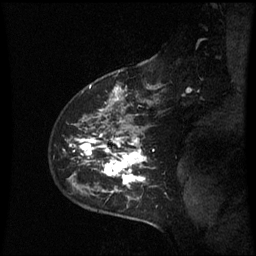
Breast MRI (dynamic contrast-enhanced), one sagittal slice; slice 46 of 60 in the series (ordered by position); dynamic contrast-enhanced series, image 2 of 3 at this slice position (ordered by acquisition); 1.5 T; TE 4.2 ms, TR 8.9 ms; 256 × 256 image matrix. Female patient, age 43 years. Case-level facts recorded for this patient, not image findings: setting: breast cancer imaged before/during neoadjuvant chemotherapy; receptor status: HER2-positive.
Outlined on this slice (semi-automatically segmented with operator editing):
- analysis volume of interest (the breast-tissue region the enhancement analysis was run in; not a lesion): bounding box <64,80,159,195> (left, top, right, bottom; pixels)
- tumour enhancement mask (voxels above the 70 % enhancement threshold inside the analysis volume of interest): <71,88,148,192>